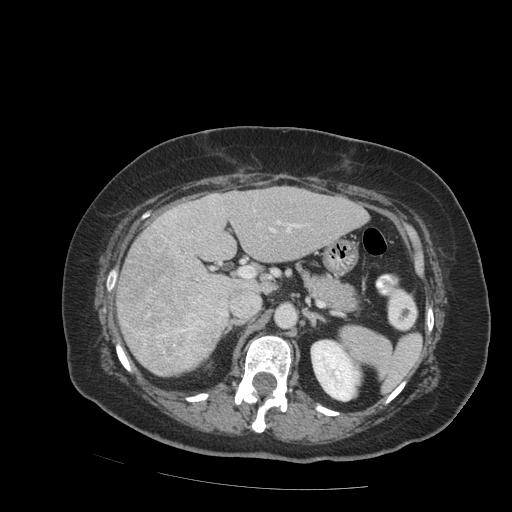
Contrast-enhanced abdominal CT (liver protocol), one axial slice. Position 46 of 99 along the scan axis. Reconstruction kernel STANDARD. Soft-tissue window (W 400 / L 40 HU). 2.5 mm slice thickness. 512 × 512 image matrix, field of view 400 × 400 mm. From the clinical record (not read from this slice): diagnosis: hepatocellular carcinoma (patient treated with transarterial chemoembolisation; whether this scan precedes or follows treatment is not stated here); TNM stage (as recorded): Stage-IVB.
Annotated regions visible in this slice (semi-automatic segmentation, software-assisted and operator-edited):
- liver parenchyma outside the tumour (the mass and vessels are separate outlines, so this box may not span the whole liver): bounding box <116,186,368,376> (left, top, right, bottom; pixels)
- mass: <117,239,229,374>
- liver vessels: <173,215,300,278>